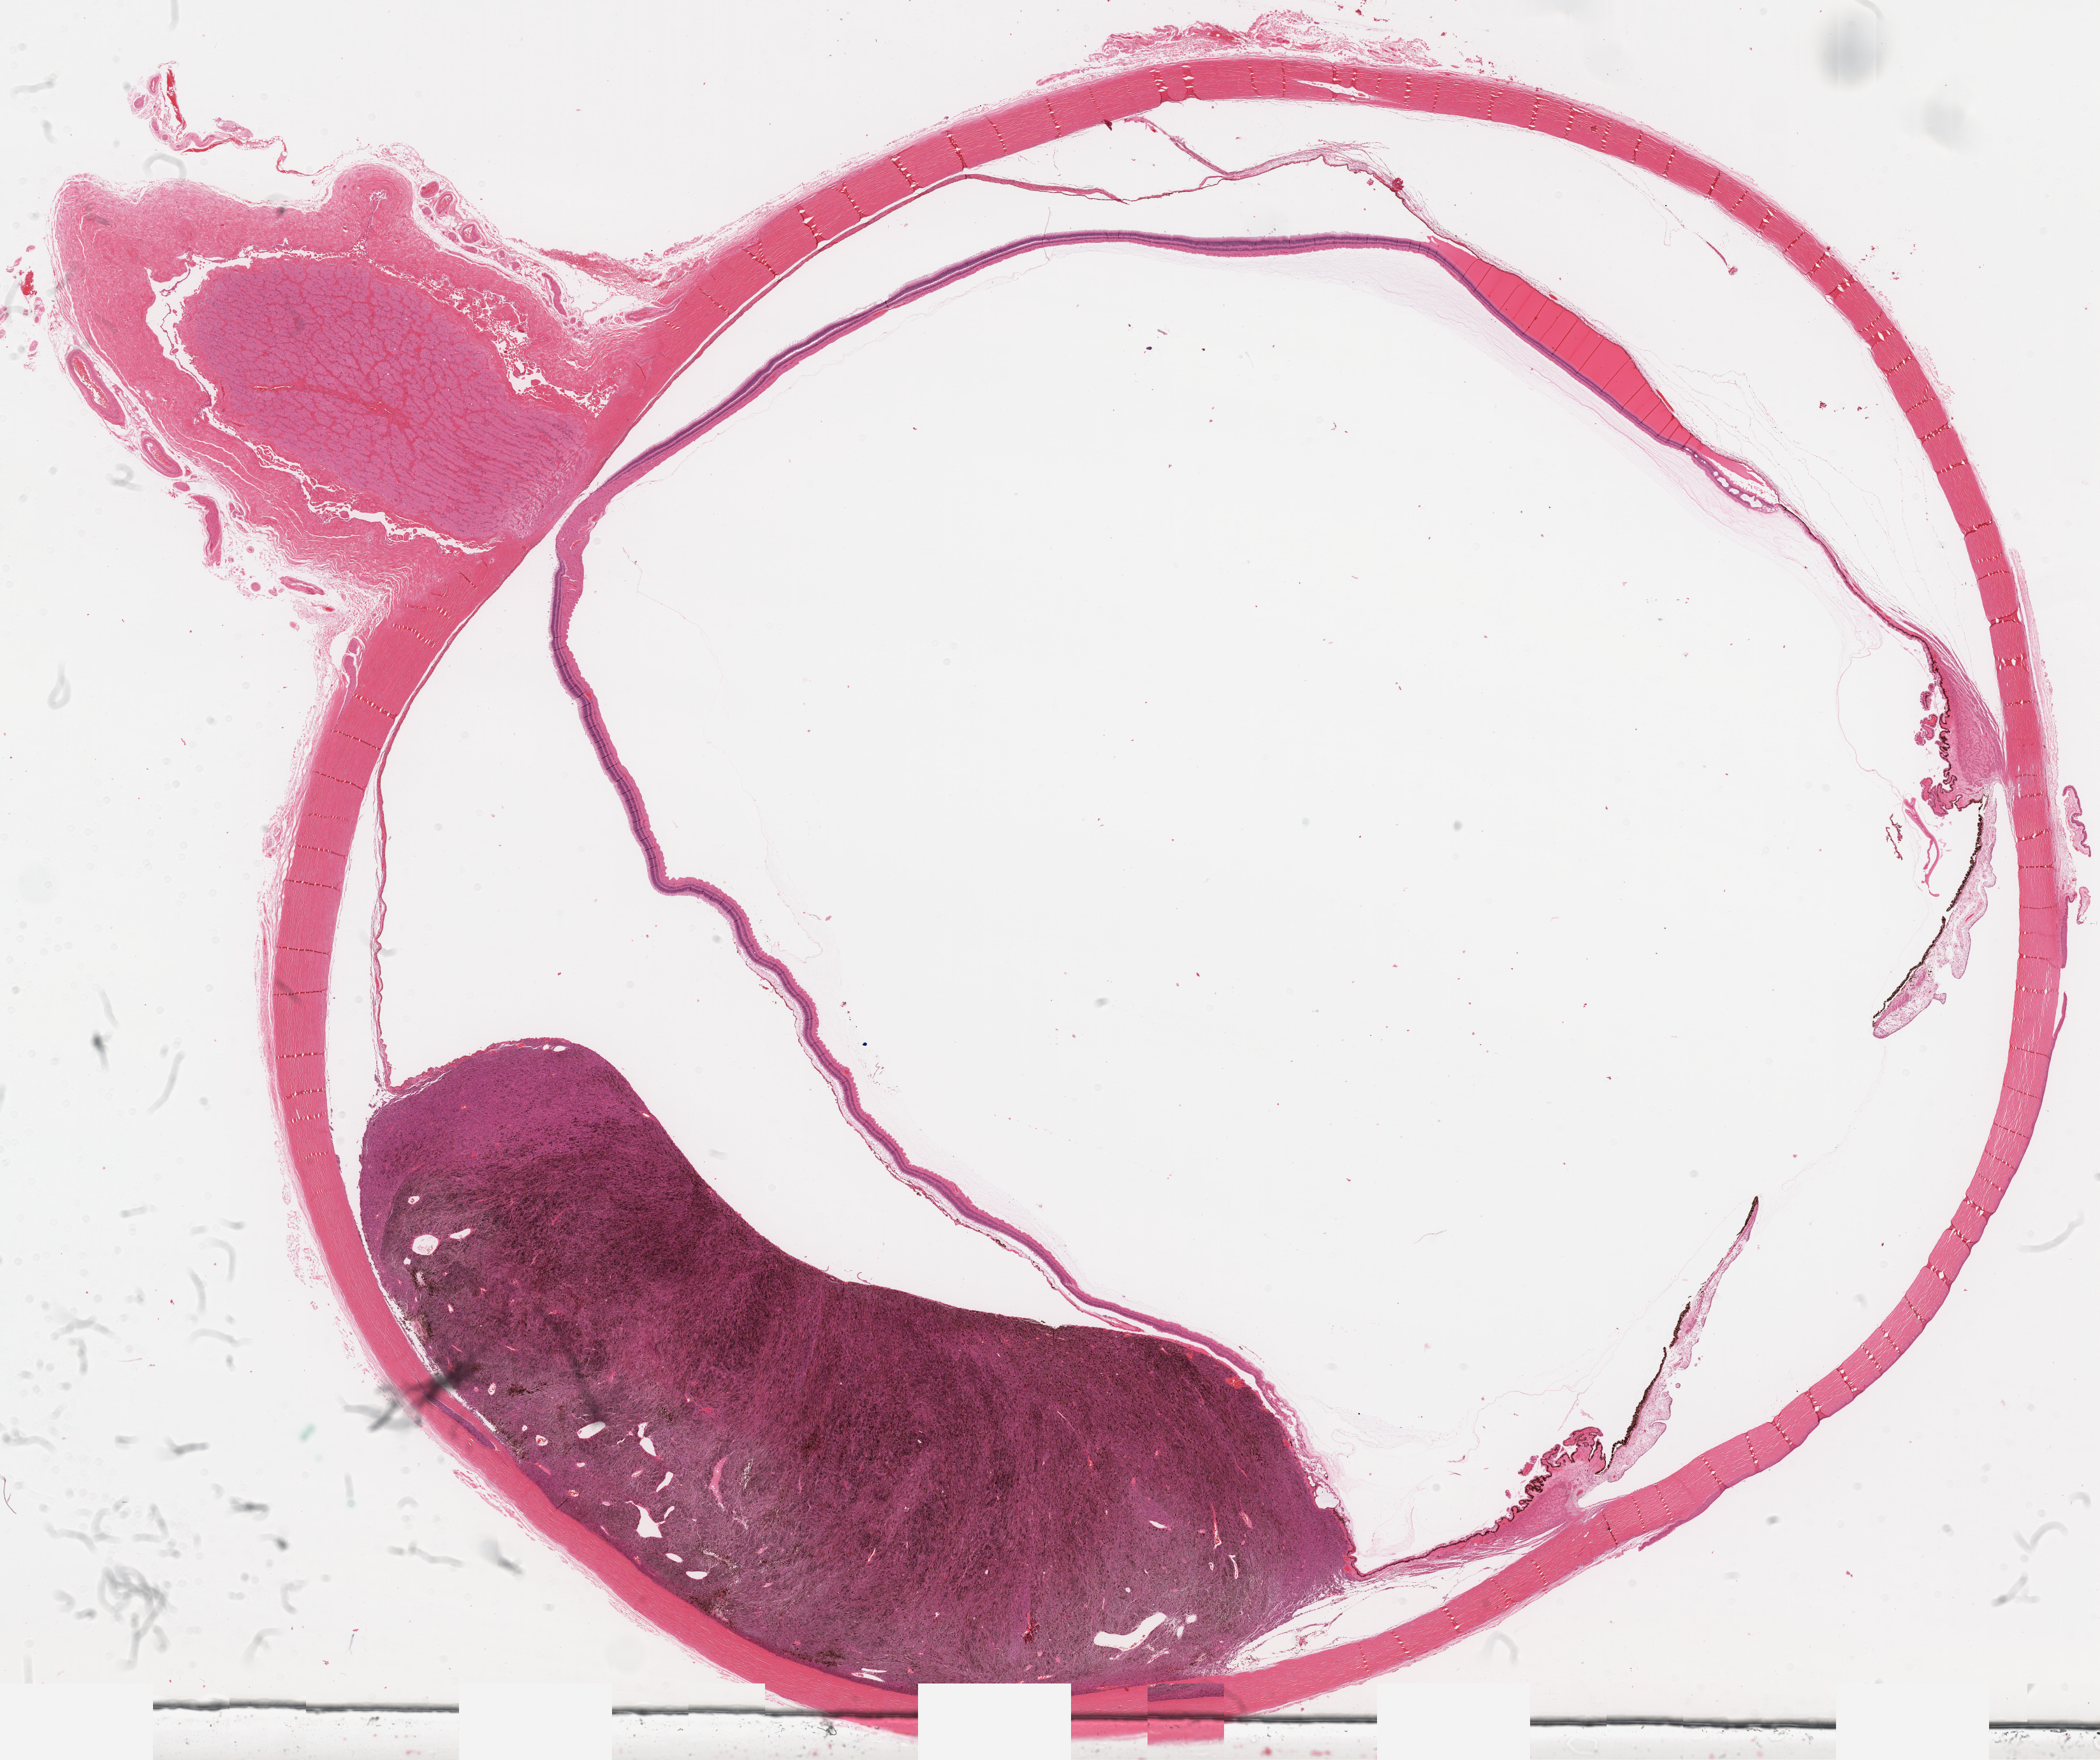
H&E-stained whole-slide image, whole scanned area (about 26.6 x 22.3 mm) shown as a low-resolution overview, formalin-fixed paraffin-embedded (FFPE) diagnostic section, sample: primary tumour, uvea. Female patient; age at initial diagnosis 77 years.
• histologic diagnosis: Mixed epithelioid and spindle cell melanoma (choroid)
• AJCC pathologic stage: IIB (7th edition)